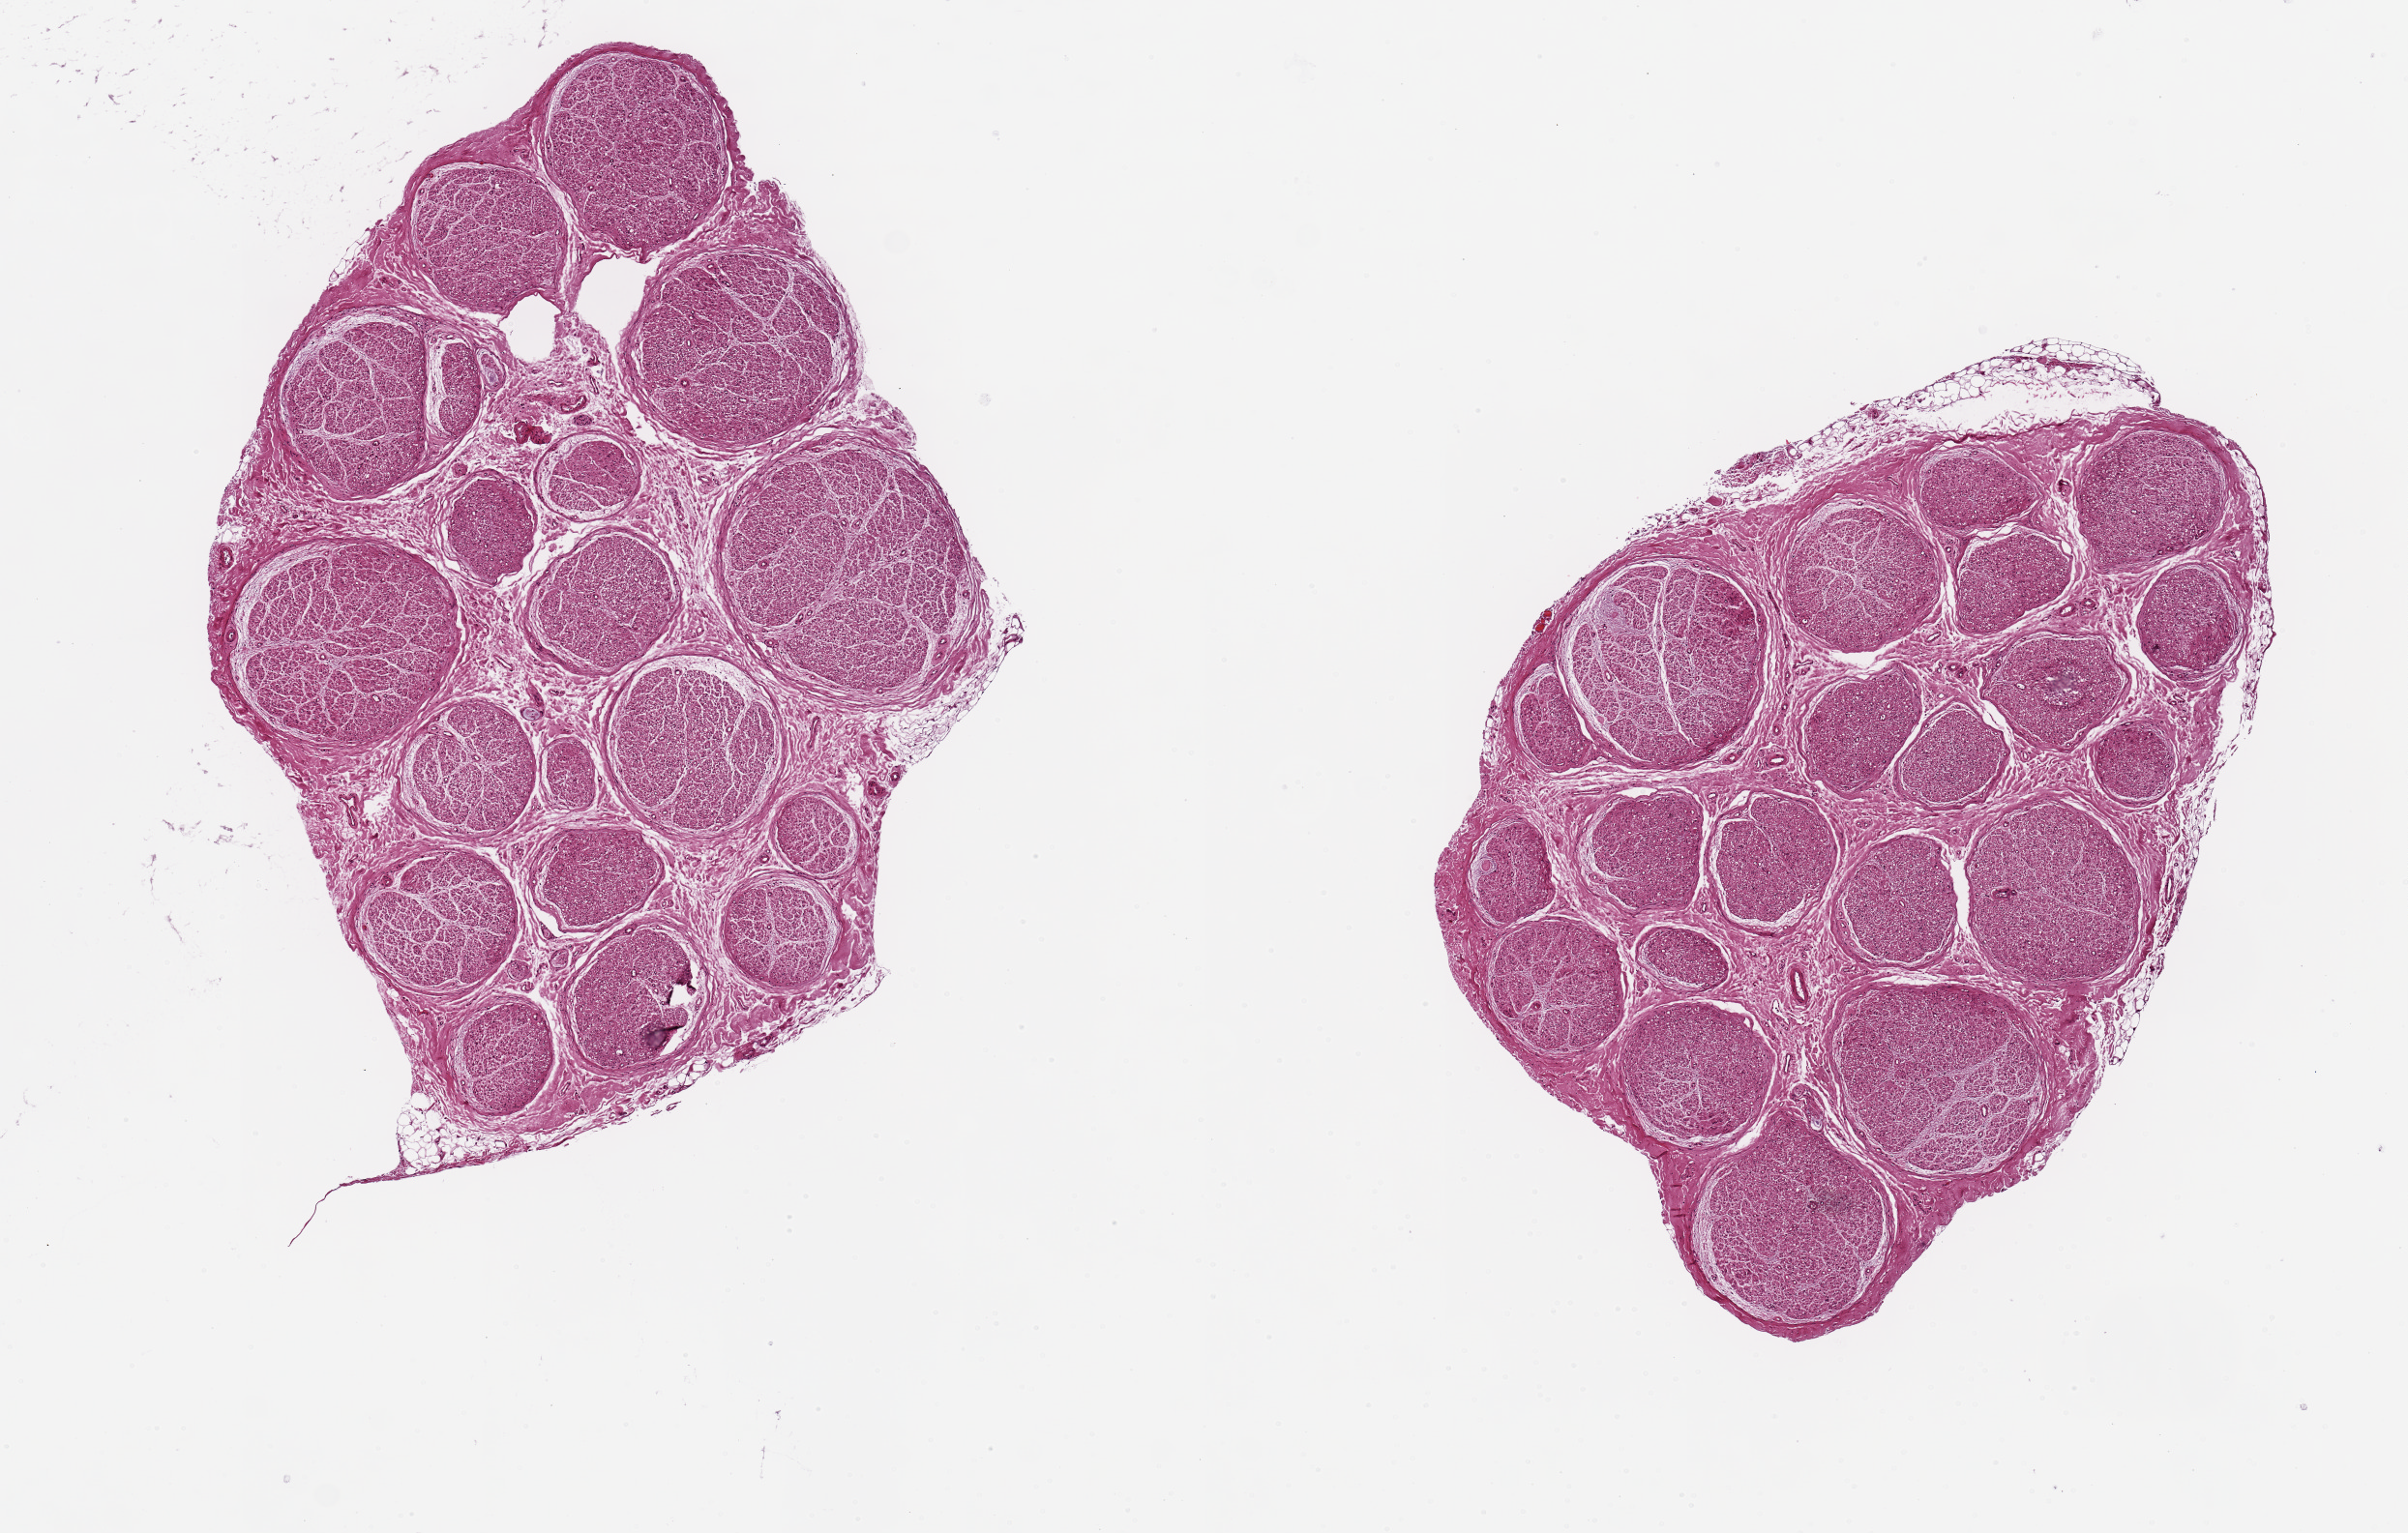
Digitized haematoxylin and eosin-stained section, brightfield — shown as a low-resolution overview of the whole scanned area (about 9.8 x 6.3 mm). PAXgene-fixed paraffin-embedded (PFPE) section. Section of tibial nerve (target tissue). Donor tissue sample. Donor sex: female.
* review note (as recorded): 2 pieces , each 3.8x3mm; minimal adipose